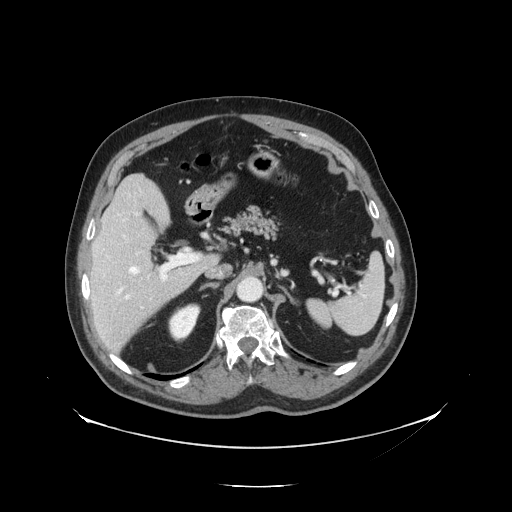
Contrast-enhanced abdominal CT, one axial slice. Slice 85 of 138 in the series (ordered by position). Reconstruction kernel STANDARD. 120 kVp. Intravenous contrast given. Soft-tissue window (W 400 / L 40 HU). 2.5 mm slice thickness. 512 × 512 image matrix. Male patient, age 77 years. From the clinical record (not read from this slice): diagnosis: colorectal cancer liver metastases, imaged before liver resection; multiple liver metastases: no; largest metastasis: 1.5 cm; disease in both lobes: no.
Annotated regions visible in this slice (expert manual segmentation):
- hepatic veins: bounding box (x1, y1, x2, y2) in pixels: (129, 266, 139, 275)
- liver: (90, 175, 216, 353)
- planned liver remnant (the part of the liver to remain after resection): (92, 175, 170, 287)
- portal vein (with intrahepatic branches): (124, 249, 200, 300)